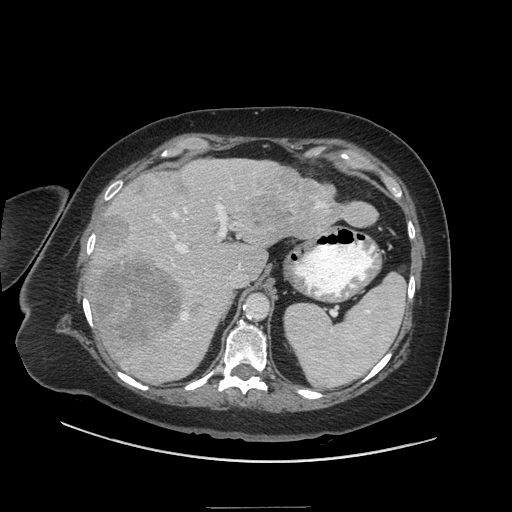
Contrast-enhanced abdominal CT (liver protocol), one axial slice. Position 36 of 81 along the scan axis. Soft-tissue window (W 400 / L 40 HU). 512 × 512 image matrix, field of view 440 × 440 mm. From the clinical record (not read from this slice): diagnosis: hepatocellular carcinoma (patient treated with transarterial chemoembolisation; whether this scan precedes or follows treatment is not stated here); TNM stage (as recorded): Stage-II; Child-Pugh class: A; tumour differentiation: moderately differentiated; tumour nodularity: multinodular.
Annotated regions visible in this slice (semi-automatic segmentation, software-assisted and operator-edited):
- liver parenchyma outside the tumour (the mass and vessels are separate outlines, so this box may not span the whole liver): bounding box (x1, y1, x2, y2) in pixels: (90, 158, 341, 382)
- mass: (95, 170, 378, 344)
- liver vessels: (130, 173, 255, 370)